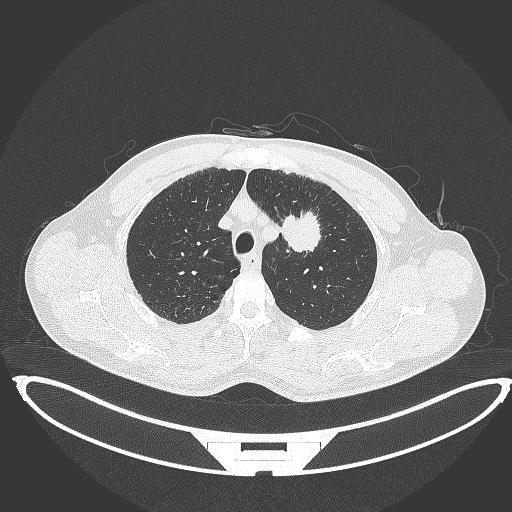
Chest CT, one axial slice. Position 348 of 395 along the scan axis. 120 kVp. Lung window (W 1500 / L -600 HU). 512 × 512 image matrix, field of view 457 × 457 mm. Male patient, age 60 years. From the clinical record (not read from this slice): clinical TNM (as recorded): T2a N0 M0; histopathological grade: G1-G2.
Outlined on this slice (bounding box drawn by a radiologist):
- lung tumour (recorded histology: squamous cell carcinoma): bounding box <280,210,322,255> (left, top, right, bottom; pixels)